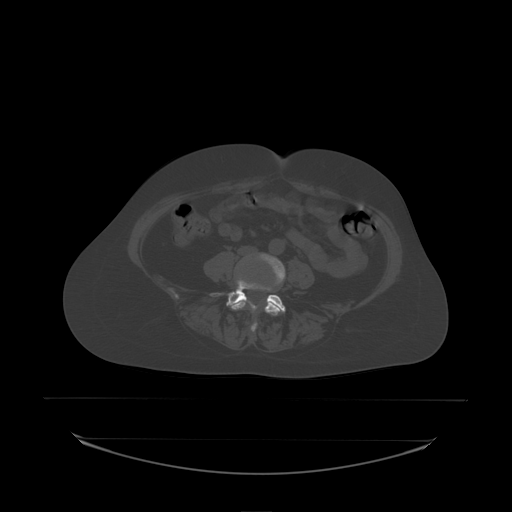
CT including the spine, one axial slice. Position 44 of 242 along the scan axis. Bone window (W 1800 / L 400 HU). 512 × 512 image matrix. Female patient, age 53 years. Case-level facts recorded for this patient, not image findings: primary cancer: lung; vertebrae with lytic lesions (as recorded): T7, L1.
Outlined on this slice (semi-automatically segmented with operator editing):
- L4 vertebra: box from (x=231, y=254) to (x=286, y=332) px
- L5 vertebra: (x=215, y=280)–(x=286, y=313)